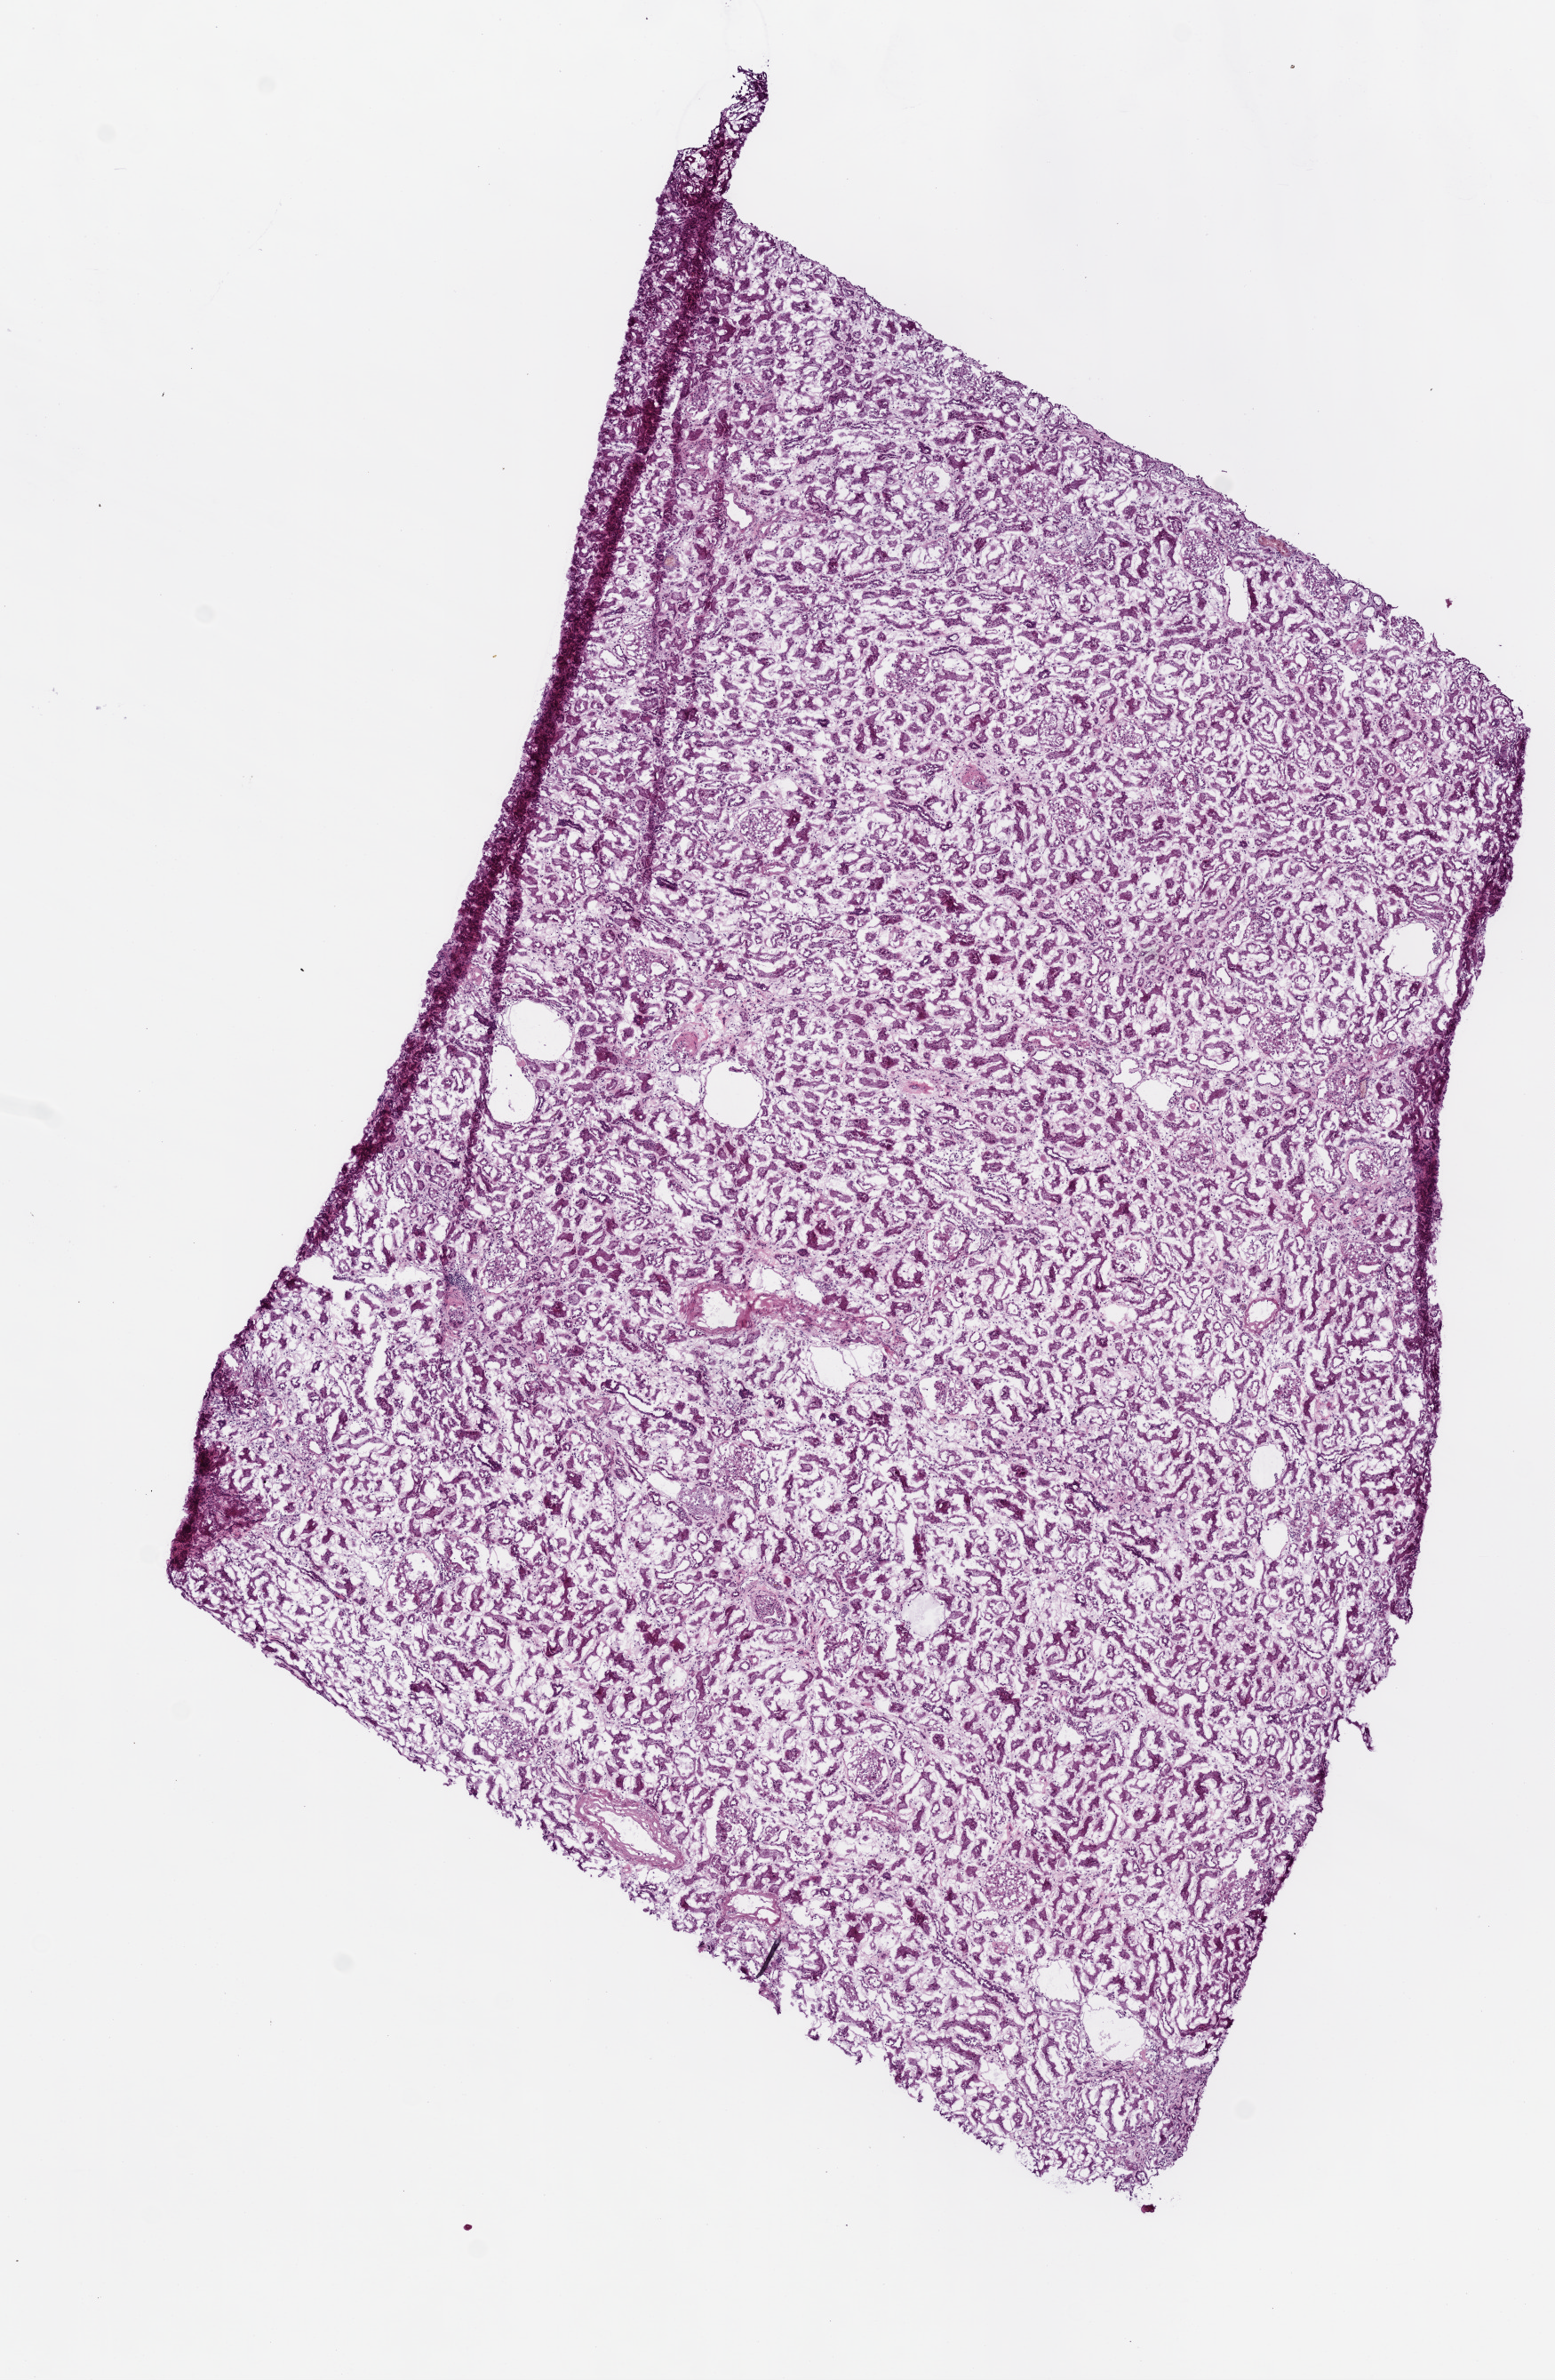
Digitized Hematoxylin and eosin (H&E) stained tissue section (whole slide), a low-resolution overview of the entire scanned area, about 7.0 x 10.7 mm (acquisition: 20x scan); frozen section; sample: solid tissue normal (non-tumour tissue), kidney. Female, age 73 years at initial diagnosis.
- this section: solid tissue normal sample (biorepository sample class)
- patient diagnosis: Clear cell adenocarcinoma, NOS